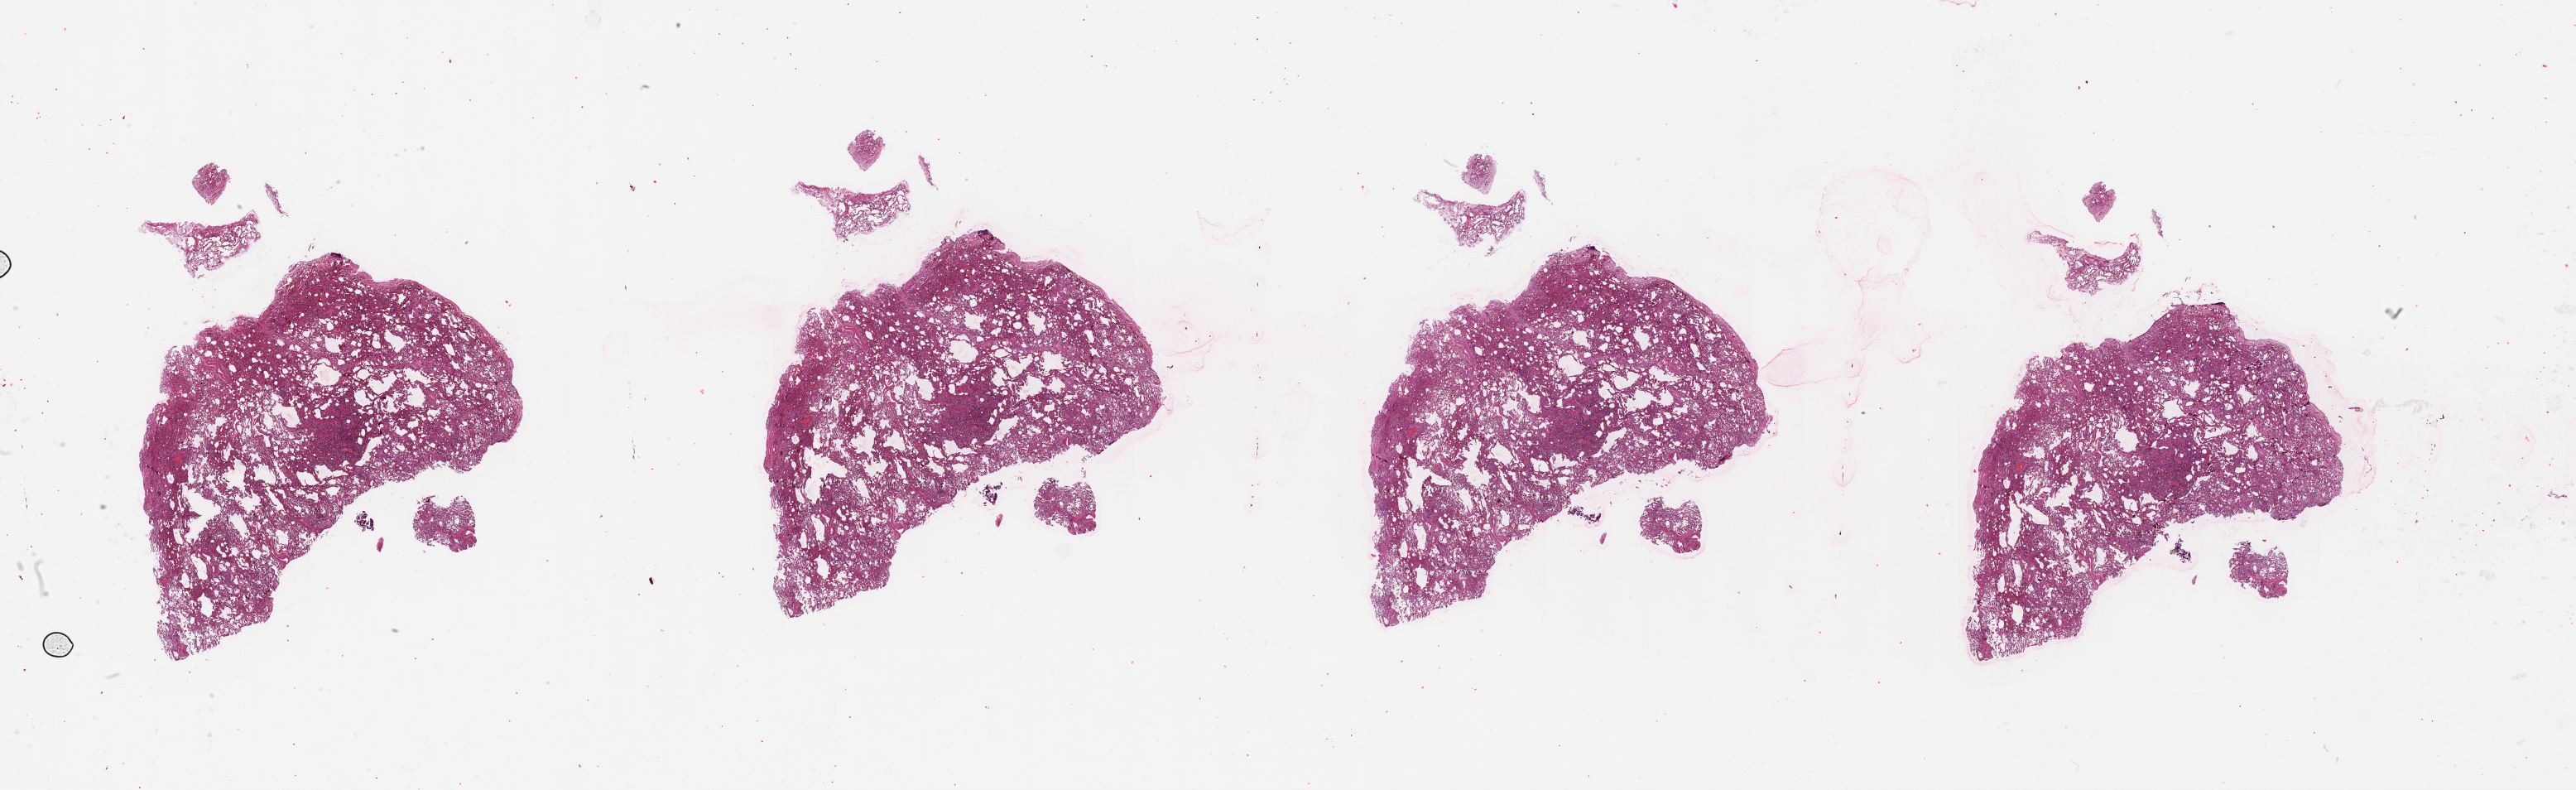
Digitized H&E-stained tissue section (whole slide), low-resolution overview of the scanned area, about 50.1 x 15.4 mm (from a 20x scan); lung, tissue type not recorded.
Patient diagnosis (cohort enrolment): lung adenocarcinoma (lung).